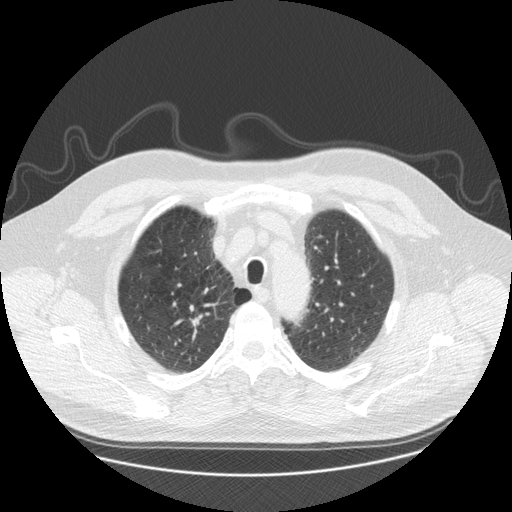
Low-dose screening chest CT, axial slice, third annual screen, lung window (W 1500 / L -600 HU), 2.5 mm slice thickness, 120 kVp, slice 32 of 173 in the series, 512 × 512 image matrix, field of view 400 × 400 mm. Male participant, aged 61 years at enrolment. Former smoker at enrolment.
Expert-annotated lung lesion, bounding box [x1, y1, x2, y2] px = [170, 303, 214, 336]. Screening reader's record for this exam (one nodule recorded; not confirmed to be the boxed lesion): non-calcified nodule or mass ≥4 mm, right upper lobe, 10 × 7 mm, smooth margins, soft tissue attenuation, pre-existing on the prior screen: yes; interval growth: yes. Official screen result: positive, other. Later outcome: lung cancer diagnosed 110 days after this screen — squamous cell carcinoma, NOS, right upper lobe, moderately differentiated (G2), stage IA (AJCC 6th edition), 10 mm at pathology.